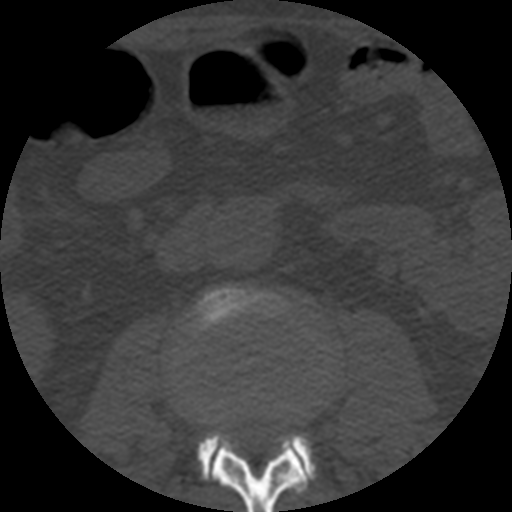
CT including the spine, one axial slice. Position 138 of 508 along the scan axis. Reconstruction kernel STANDARD. 120 kVp. Bone window (W 1800 / L 400 HU). 1.25 mm slice thickness. 512 × 512 image matrix, field of view 160 × 160 mm. Patient age 57 years. Case-level facts recorded for this patient, not image findings: primary cancer: prostate.
Structures marked on this image (semi-automatically segmented with operator editing):
- L2 vertebra: box from (x=202, y=433) to (x=311, y=512) px
- L3 vertebra: (x=177, y=287)–(x=316, y=479)